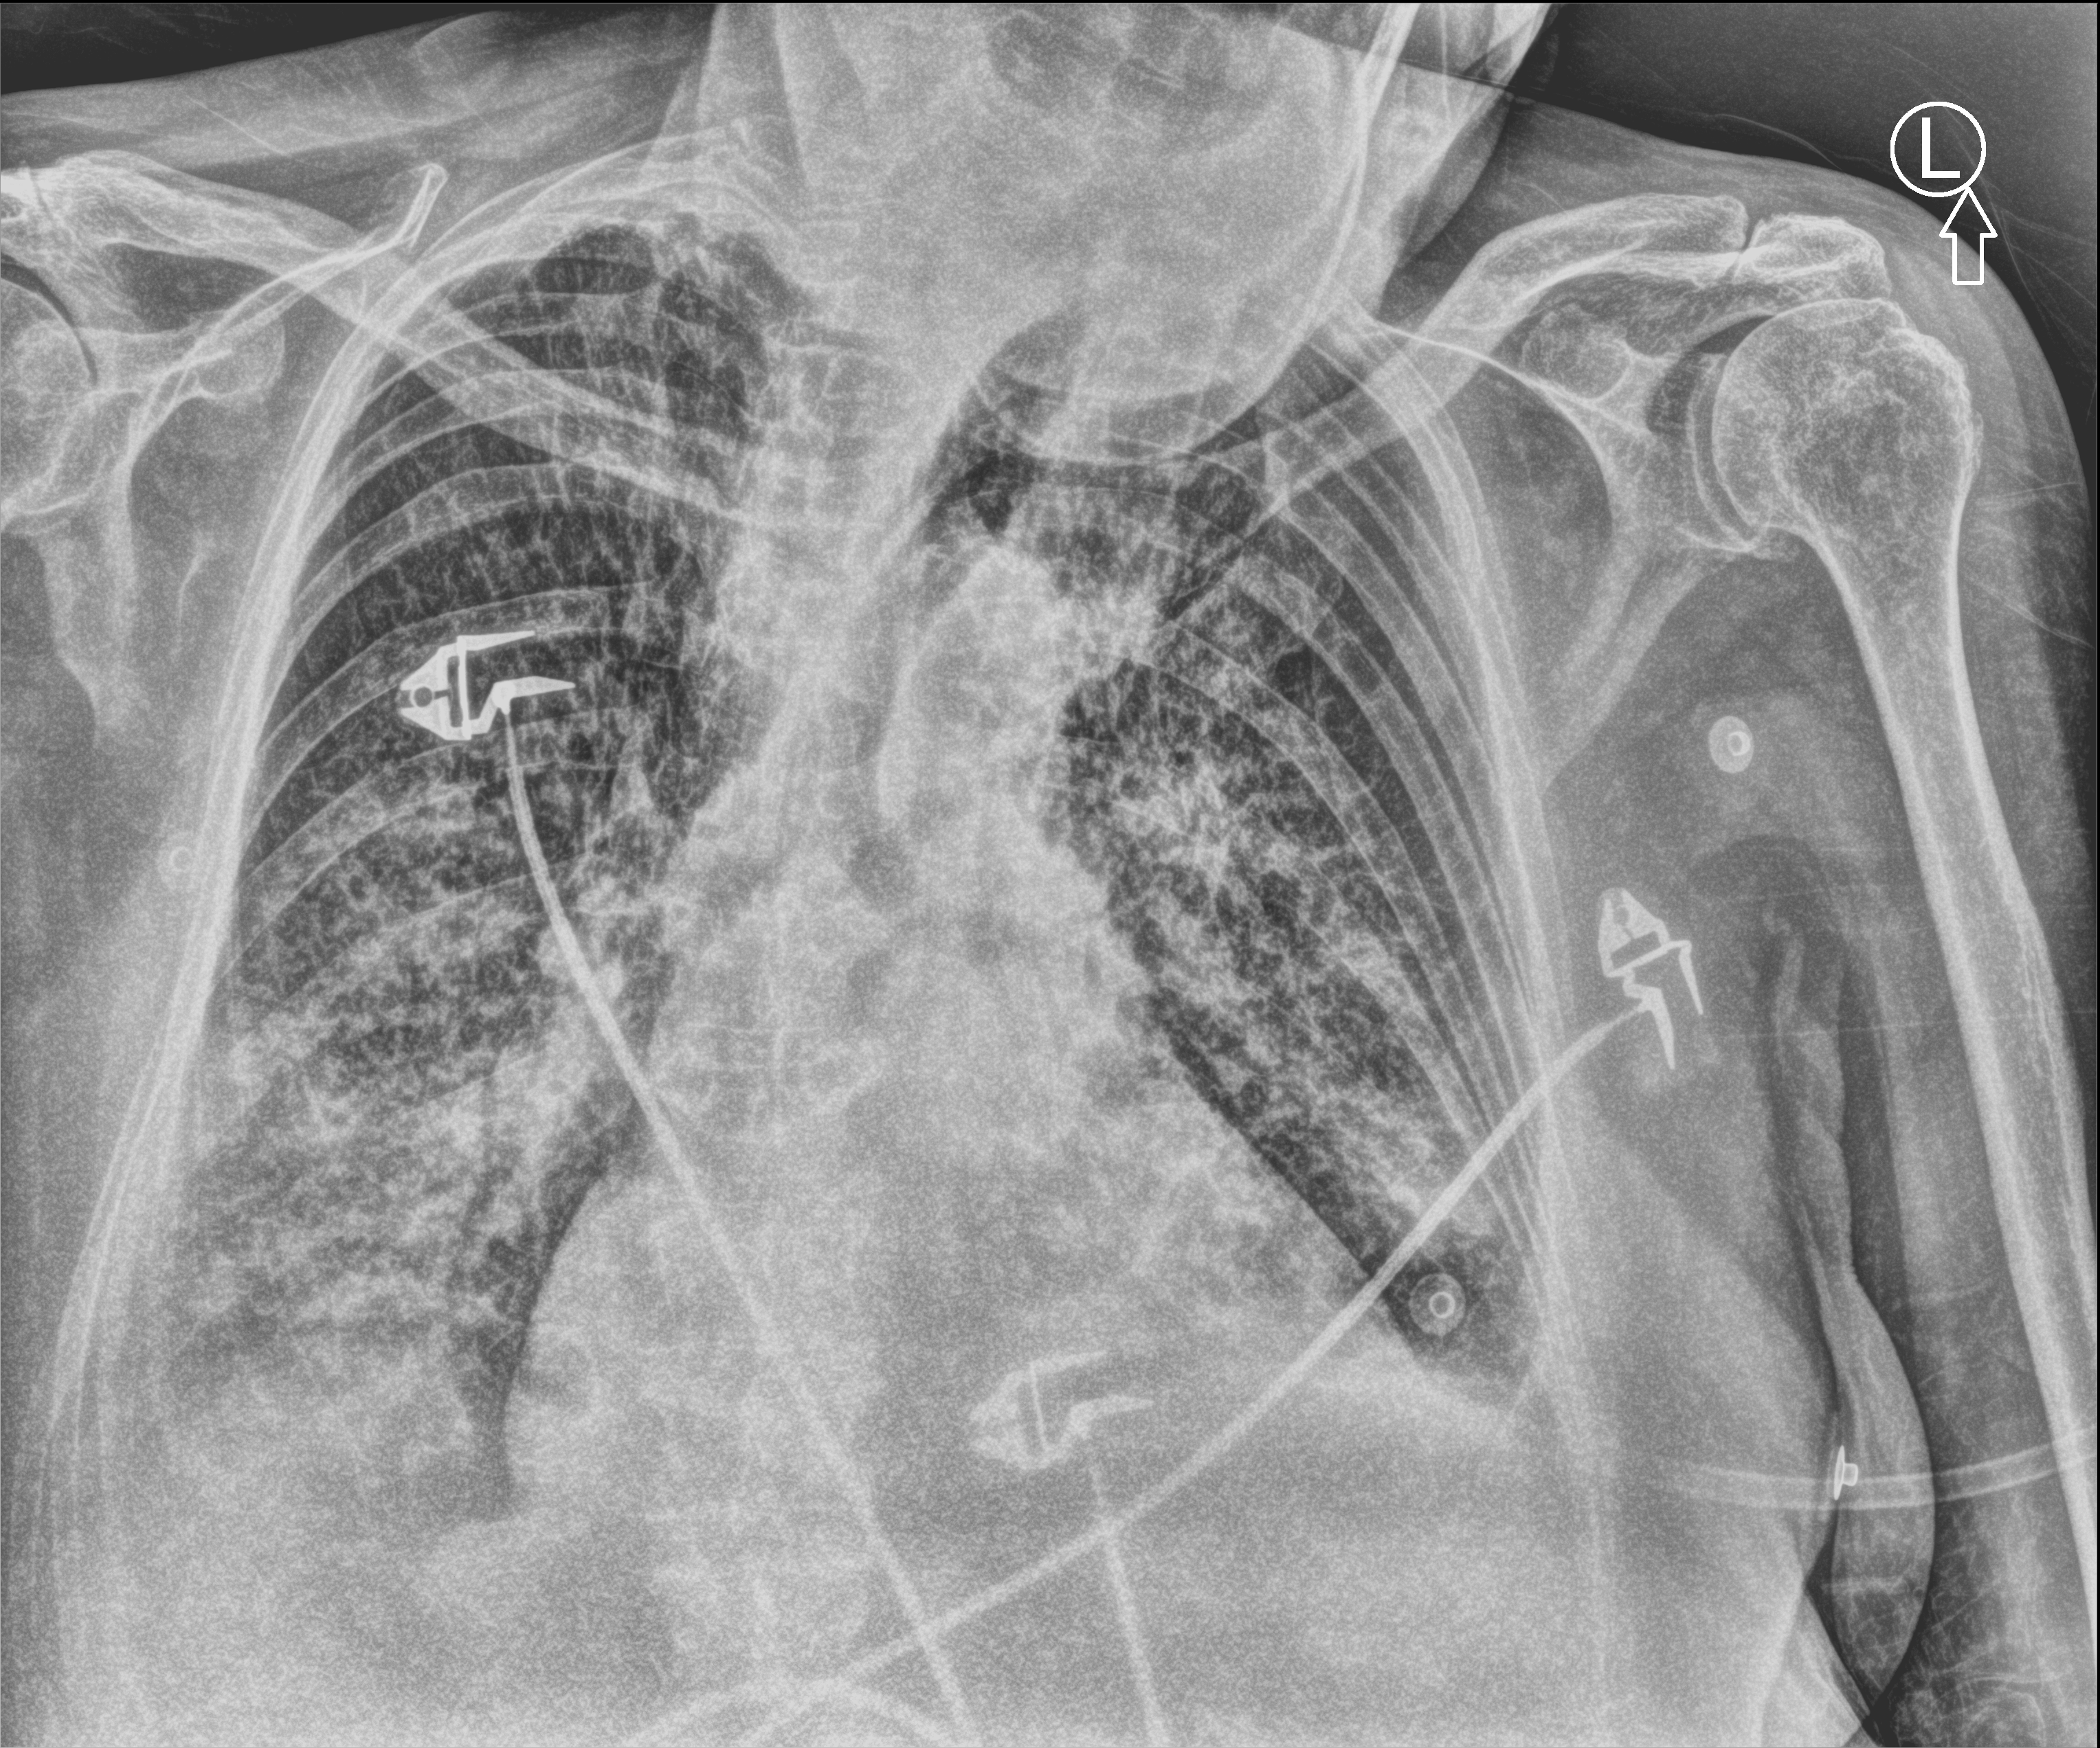
Portable chest radiograph. Male patient hospitalised with COVID-19, age 75–90 years.
From the hospital-stay record, not from the radiograph (when in the stay this image was taken is not recorded): smoking status (admission record): former; hypertension (admission record): yes; admitted to intensive care during this hospital stay: no.